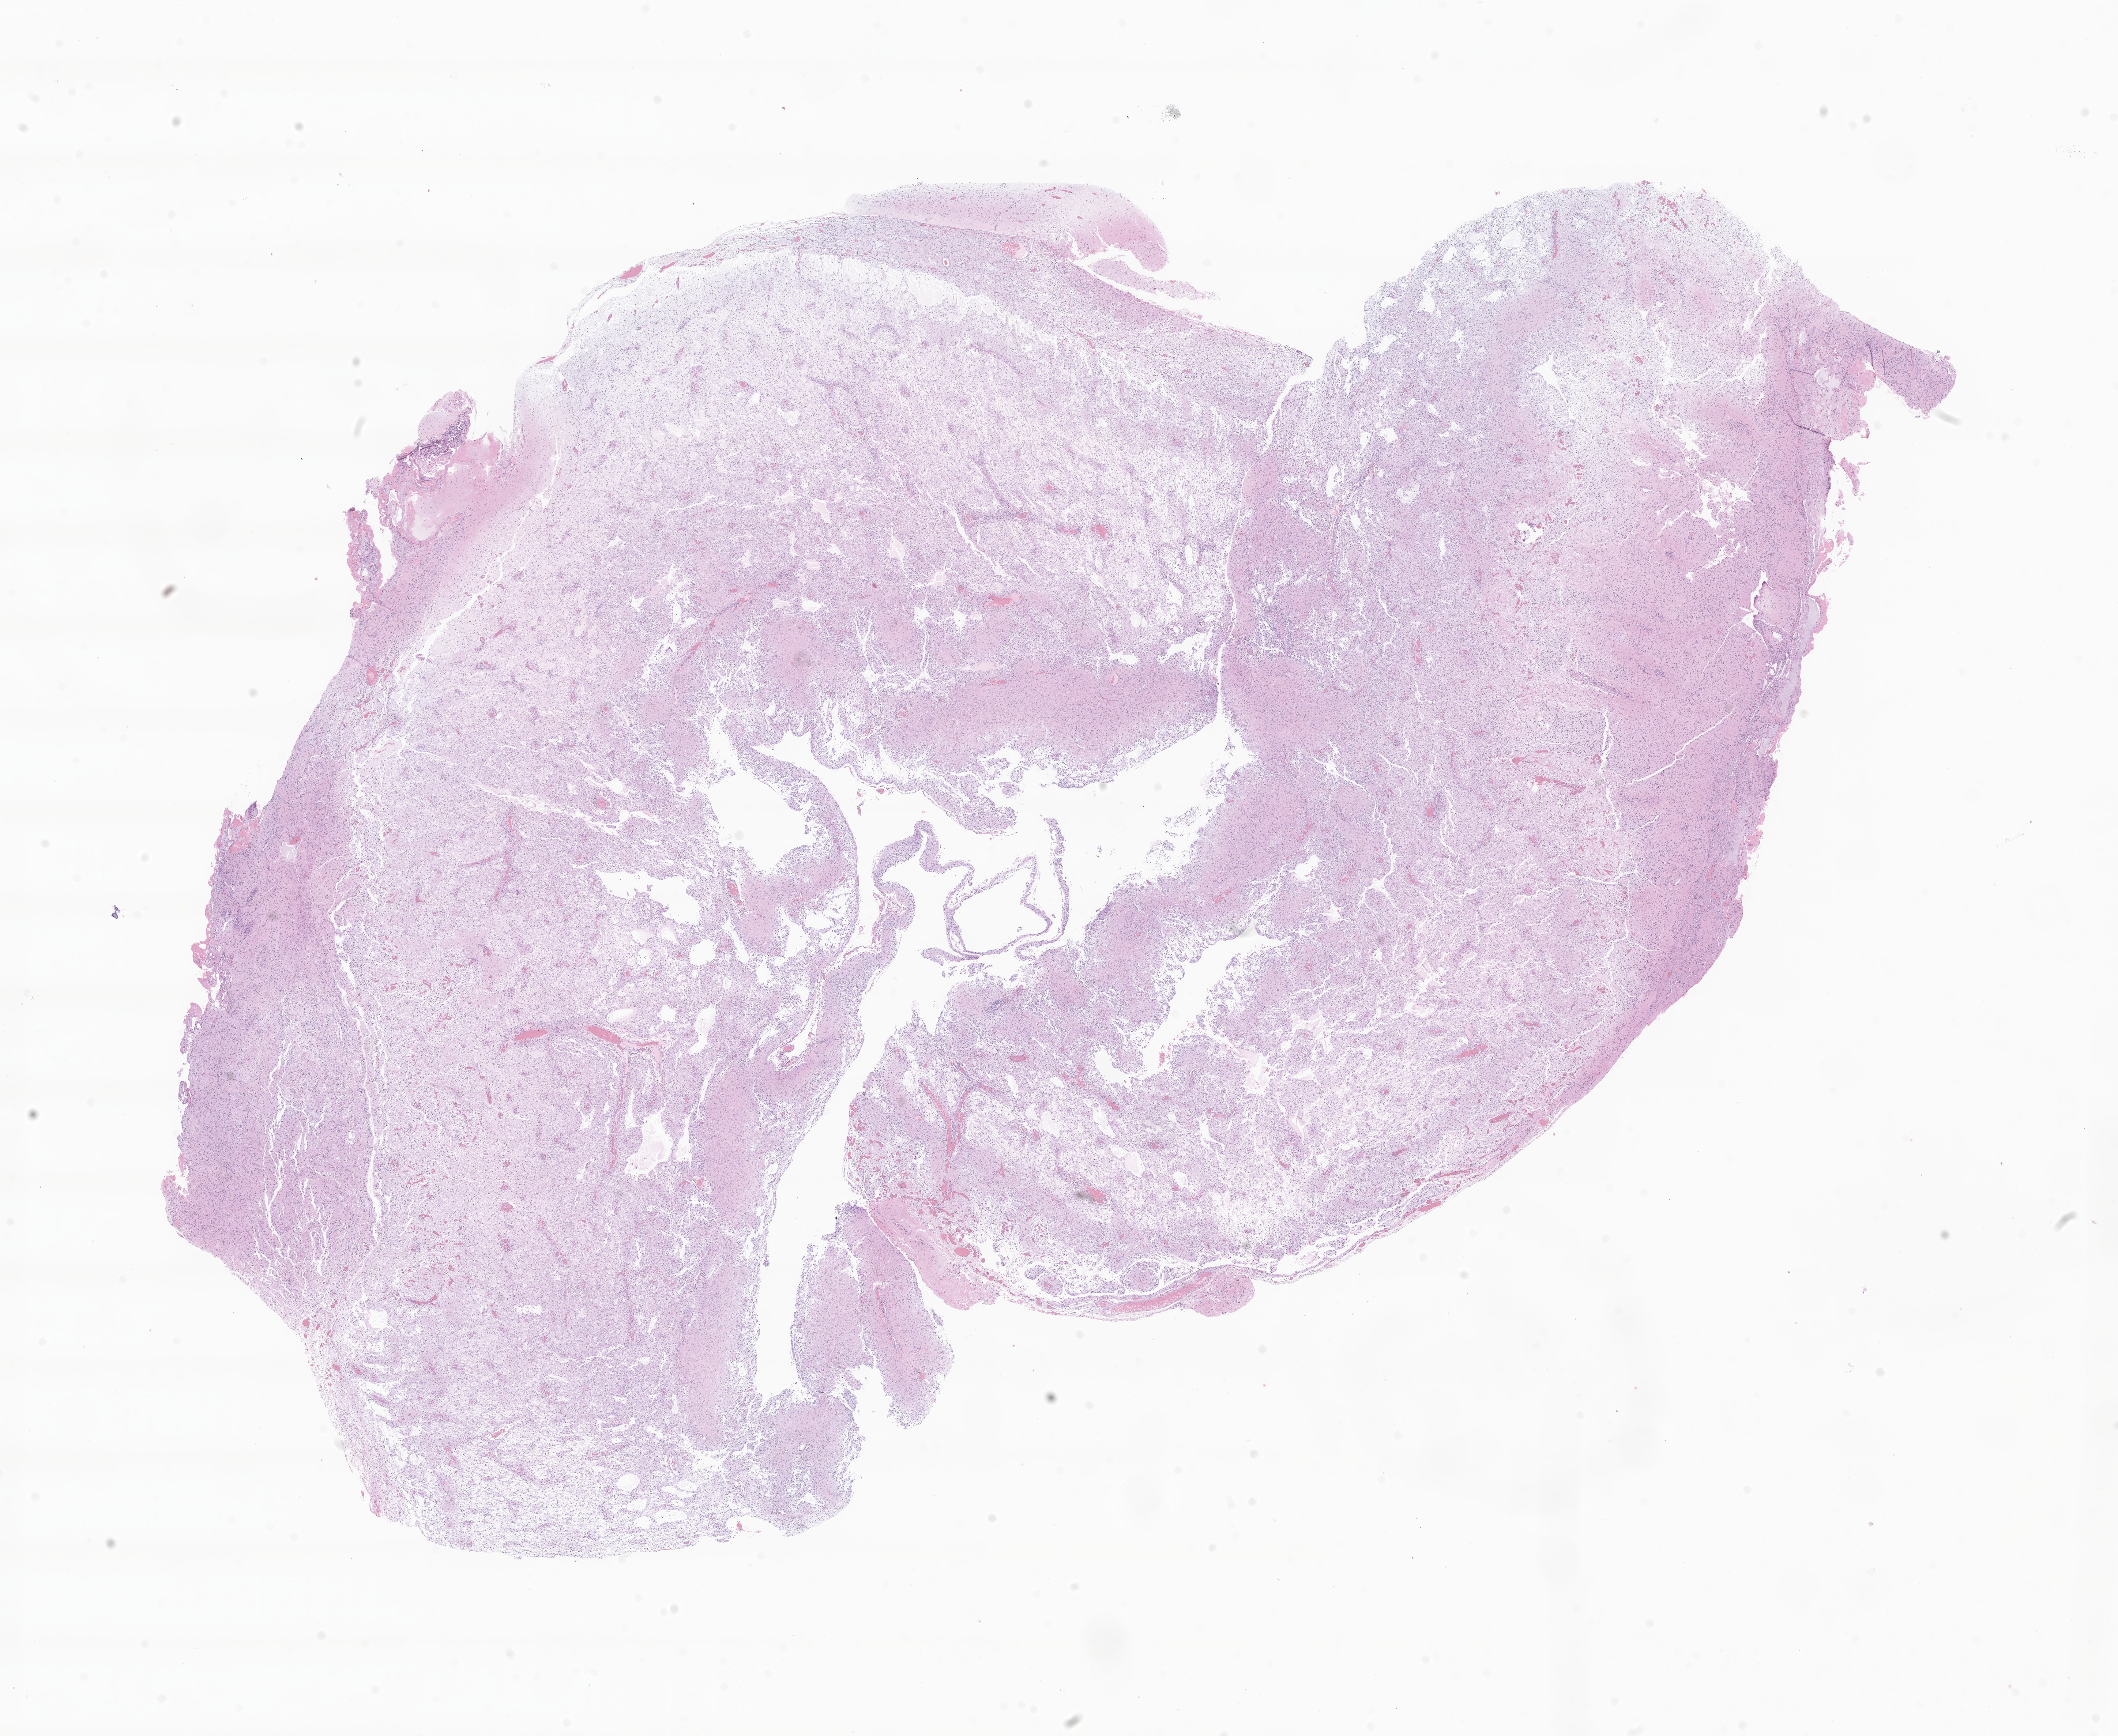
H&E whole-slide image of tumor tissue from the brain — low-resolution overview of the scanned area, about 24.4 x 20.0 mm, formalin-fixed paraffin-embedded section. Female patient, age 38 months (3 years 2 months).
Diagnosis (ICD-O-3 morphology term): Pilocytic astrocytoma.